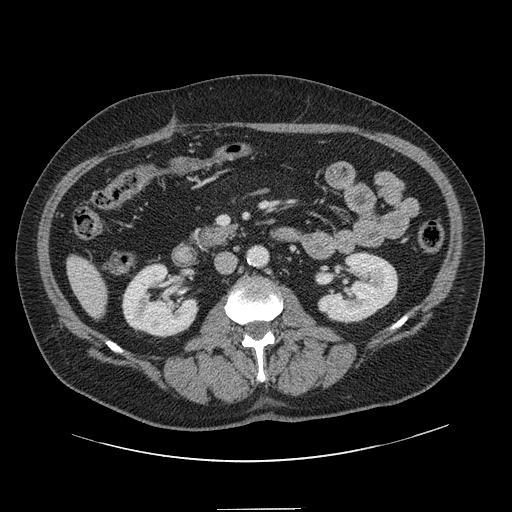
Contrast-enhanced abdominal CT, one axial slice; slice 39 of 154 in the series (ordered by position); intravenous contrast given; soft-tissue window (W 400 / L 40 HU); 2.5 mm slice thickness; 512 × 512 image matrix. Male patient, age 61 years. Case-level facts recorded for this patient, not image findings: diagnosis: colorectal cancer liver metastases, imaged before liver resection; multiple liver metastases: yes; largest metastasis: 2.6 cm.
Annotated regions visible in this slice (expert manual segmentation):
- liver: bounding box <68,257,107,317> (left, top, right, bottom; pixels)
- planned liver remnant (the part of the liver to remain after resection): <68,256,107,317>